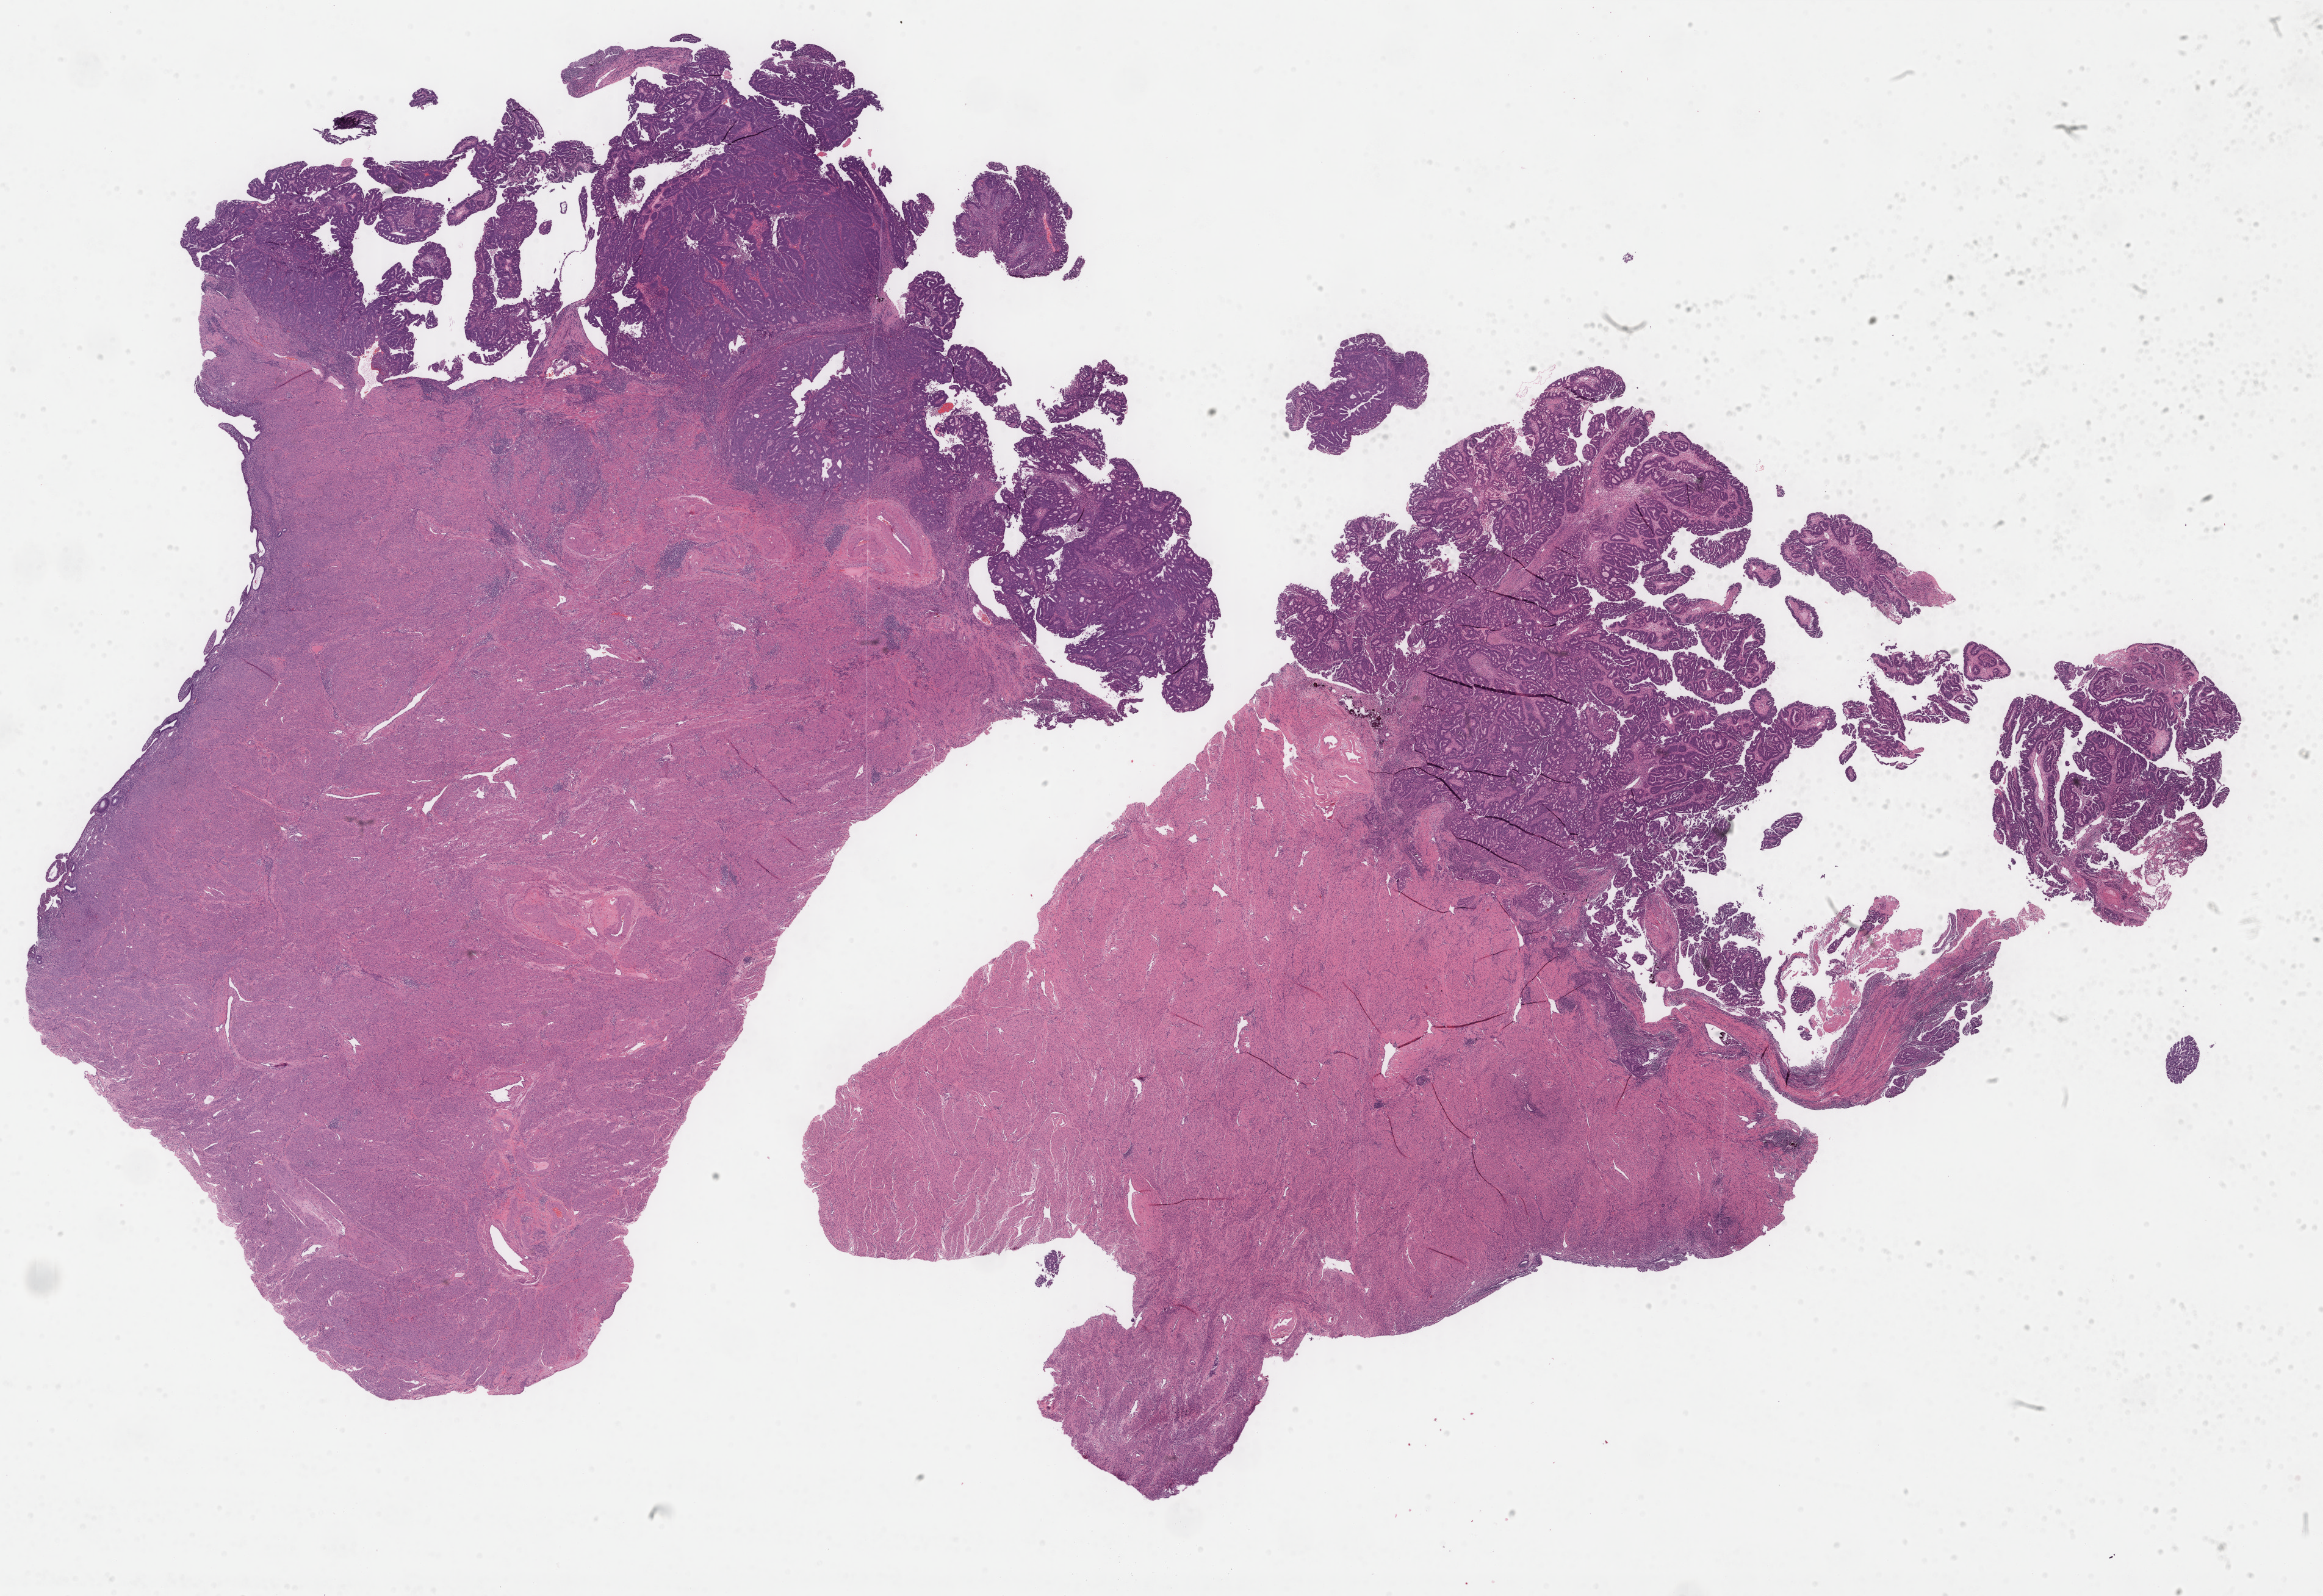
Digitized H&E-stained tissue section (whole slide) — whole scanned area (about 30.2 x 20.8 mm, acquisition: 40x scan) shown as a low-resolution overview, formalin-fixed paraffin-embedded (FFPE) diagnostic section, uterus, primary tumour sample. Female patient; age at initial diagnosis 70 years.
Pathologic diagnosis: Endometrioid adenocarcinoma, NOS (endometrium).